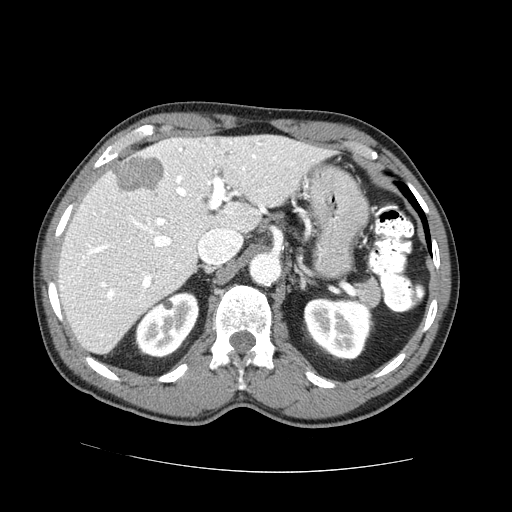
Contrast-enhanced abdominal CT (liver protocol), one axial slice. Slice 47 of 73 in the series (ordered by position). Reconstruction kernel STANDARD. One of 2 acquisitions stored at this slice position. Soft-tissue window (W 400 / L 40 HU). 2.5 mm slice thickness. 512 × 512 image matrix, field of view 380 × 380 mm. Case-level facts recorded for this patient, not image findings: diagnosis: hepatocellular carcinoma (patient treated with transarterial chemoembolisation; whether this scan precedes or follows treatment is not stated here); TNM stage (as recorded): Stage-IVA; Child-Pugh class: A; tumour nodularity: uninodular.
Outlined on this slice (semi-automatic segmentation, software-assisted and operator-edited):
- liver parenchyma outside the tumour (the mass and vessels are separate outlines, so this box may not span the whole liver): box from (x=58, y=134) to (x=327, y=354) px
- mass: (x=112, y=157)–(x=162, y=190)
- liver vessels: (x=62, y=140)–(x=277, y=300)